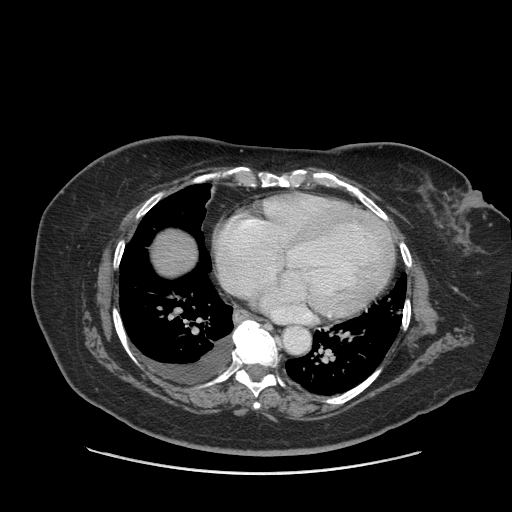
Contrast-enhanced abdominal CT (liver protocol), one axial slice. Position 87 of 91 along the scan axis. Reconstruction kernel STANDARD. Soft-tissue window (W 400 / L 40 HU). 2.5 mm slice thickness. 512 × 512 image matrix, field of view 420 × 420 mm. Case-level facts recorded for this patient, not image findings: diagnosis: hepatocellular carcinoma (patient treated with transarterial chemoembolisation; whether this scan precedes or follows treatment is not stated here); TNM stage (as recorded): Stage-I; Child-Pugh class: A; tumour differentiation: well differentiated; tumour nodularity: uninodular.
Outlined on this slice (semi-automatic segmentation, software-assisted and operator-edited):
- liver parenchyma outside the tumour (the mass and vessels are separate outlines, so this box may not span the whole liver): box from (x=152, y=228) to (x=196, y=276) px